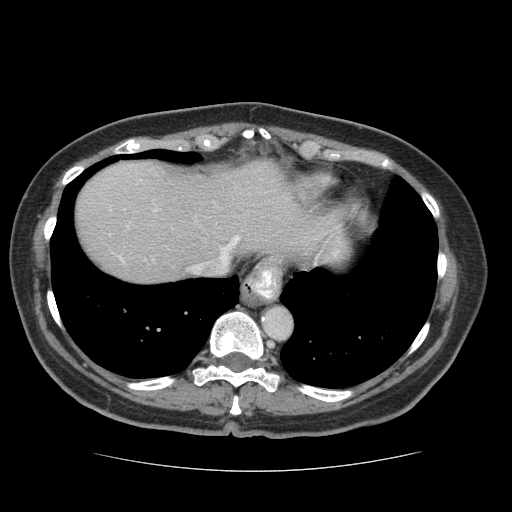
Contrast-enhanced abdominal CT (liver protocol), one axial slice; slice 62 of 75 in the series (ordered by position); 140 kVp; soft-tissue window (W 400 / L 40 HU); 2.5 mm slice thickness; 512 × 512 image matrix, field of view 360 × 360 mm. From the clinical record (not read from this slice): diagnosis: hepatocellular carcinoma (patient treated with transarterial chemoembolisation; whether this scan precedes or follows treatment is not stated here); TNM stage (as recorded): Stage-I; Child-Pugh class: A; tumour differentiation: moderately differentiated; tumour nodularity: uninodular.
Outlined on this slice (semi-automatic segmentation, software-assisted and operator-edited):
- abdominal aorta: bounding box <263,307,291,338> (left, top, right, bottom; pixels)
- liver parenchyma outside the tumour (the mass and vessels are separate outlines, so this box may not span the whole liver): <76,160,349,282>
- liver vessels: <118,208,338,263>